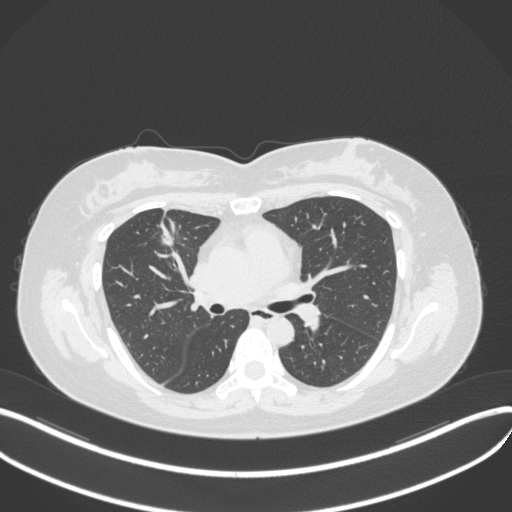
Chest CT, one axial slice. Position 188 of 272 along the scan axis. Reconstruction kernel B31f. 120 kVp. Lung window (W 1500 / L -600 HU). 512 × 512 image matrix. Patient: female, 42 years. Case-level facts recorded for this patient, not image findings: clinical TNM (as recorded): T1b N0 M0.
Structures marked on this image (rectangle marked by the reading radiologist):
- lung tumour (recorded histology: adenocarcinoma): bounding box [x1, y1, x2, y2] px = [155, 221, 181, 252]